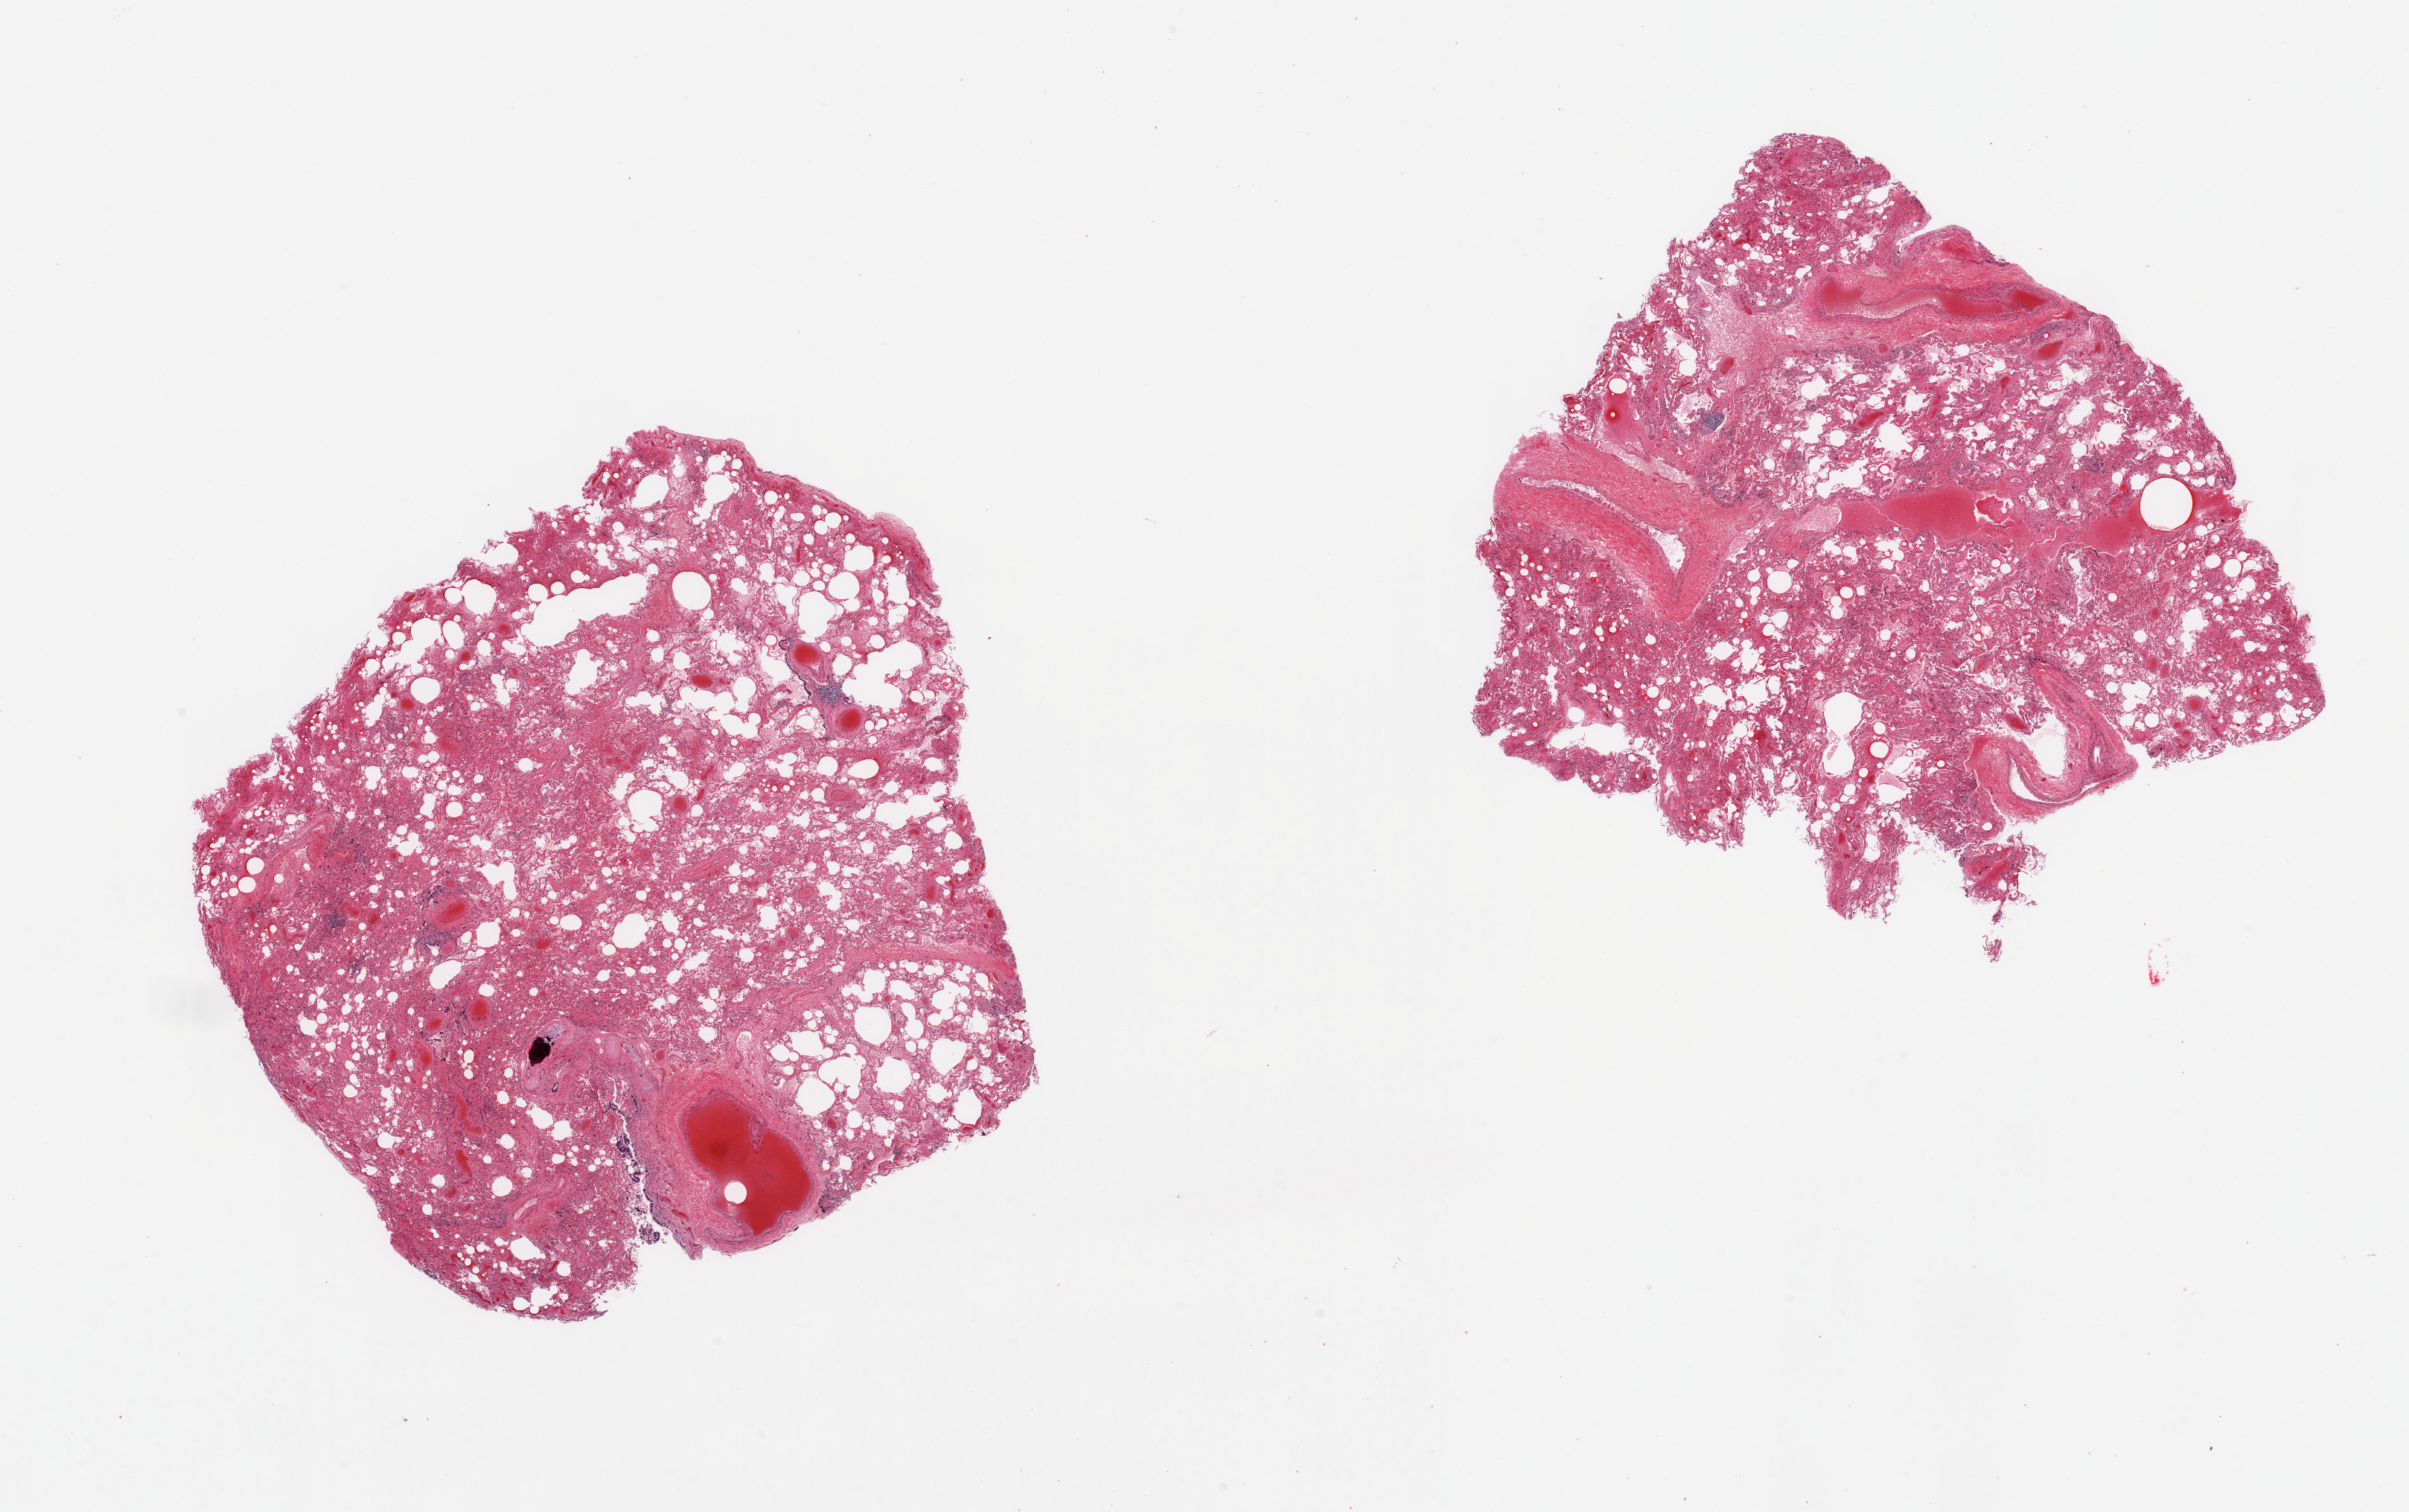
Digitized H&E-stained section — low-resolution overview of the scanned area, about 25.6 x 16.1 mm (acquisition: 20x scan); PAXgene-fixed paraffin-embedded (PFPE) section; section of lung (target tissue); donor tissue sample. Donor sex: female.
Pathologist's review note for this sample: 2 pieces; include large vessels, cartilage (not target), some congestion, edema.